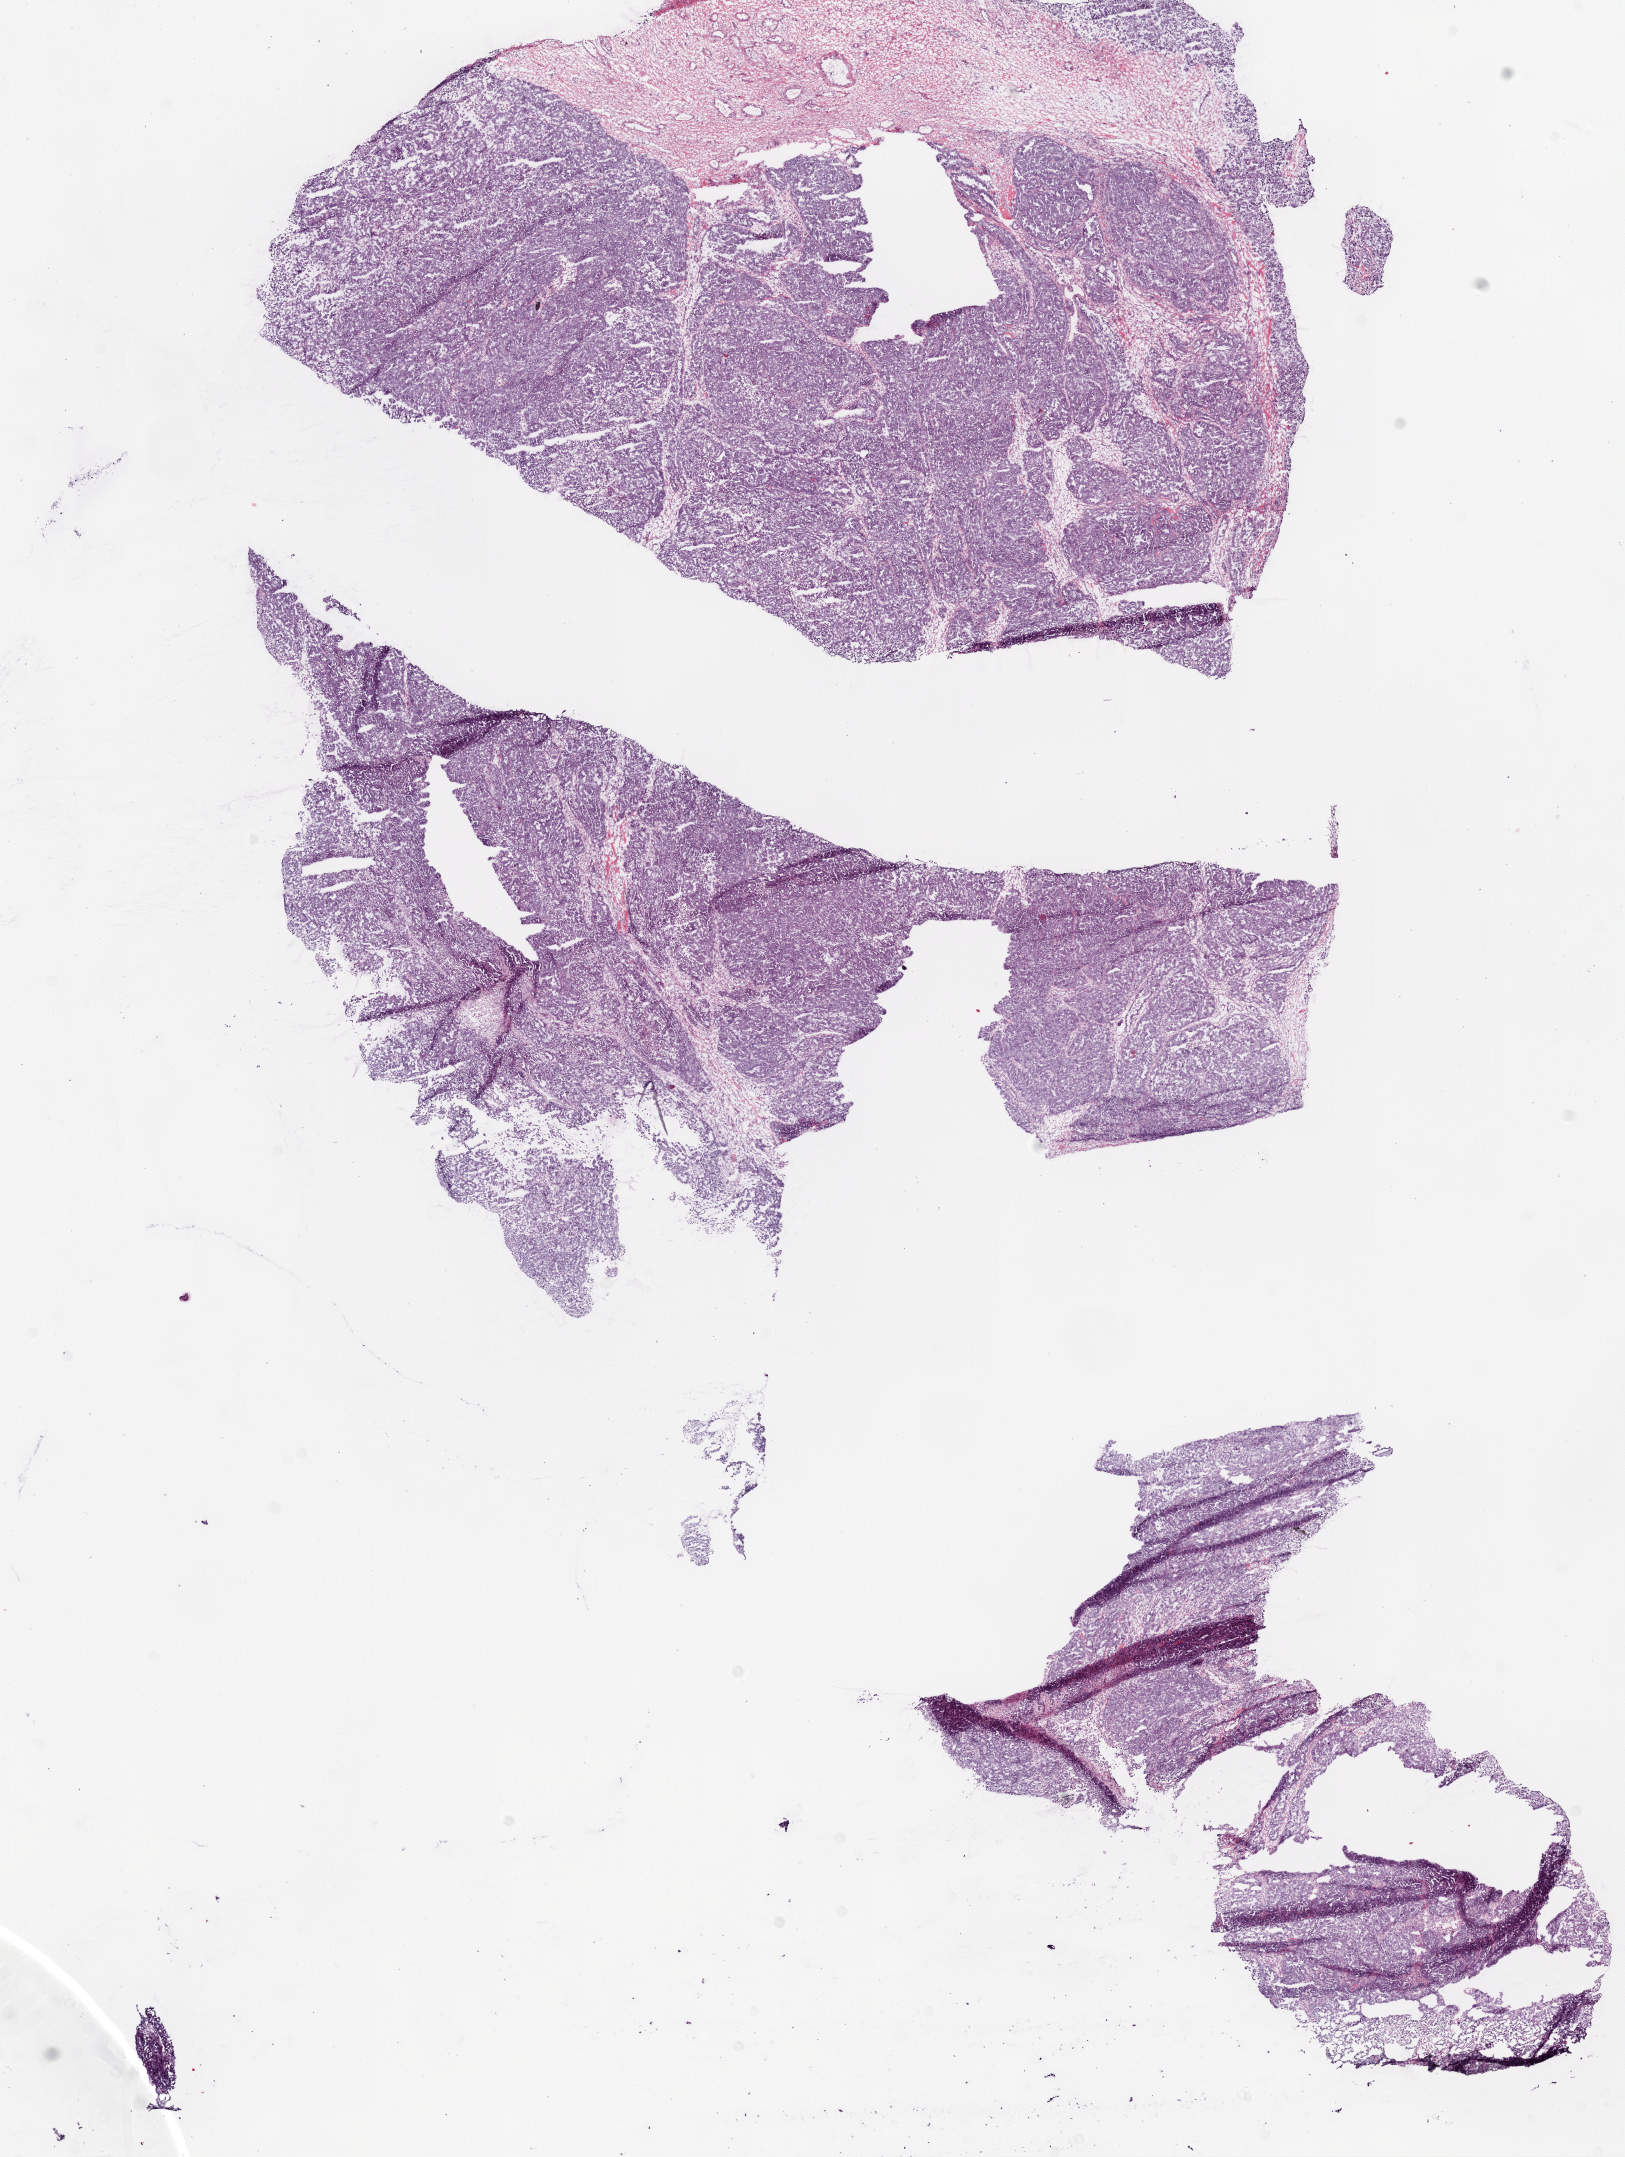
H&E whole-slide image — whole scanned area (about 13.0 x 17.3 mm, slide scanned at 20x) shown as a low-resolution overview, frozen section from the bottom of the tissue portion, primary tumour sample from the ovary. Patient: female, age at initial diagnosis 62 years. Histologic grade: G3 (poorly differentiated). Pathologist review of this section (percent, as recorded): tumour cells 80%, tumour nuclei 80%, normal cells 0%, stromal cells 20%, necrosis 0%. Inflammatory infiltration, as recorded: lymphocyte infiltration 0%, monocyte infiltration 0%, neutrophil infiltration 0%.
Pathologic diagnosis: Serous cystadenocarcinoma, NOS. FIGO stage: IIIC.